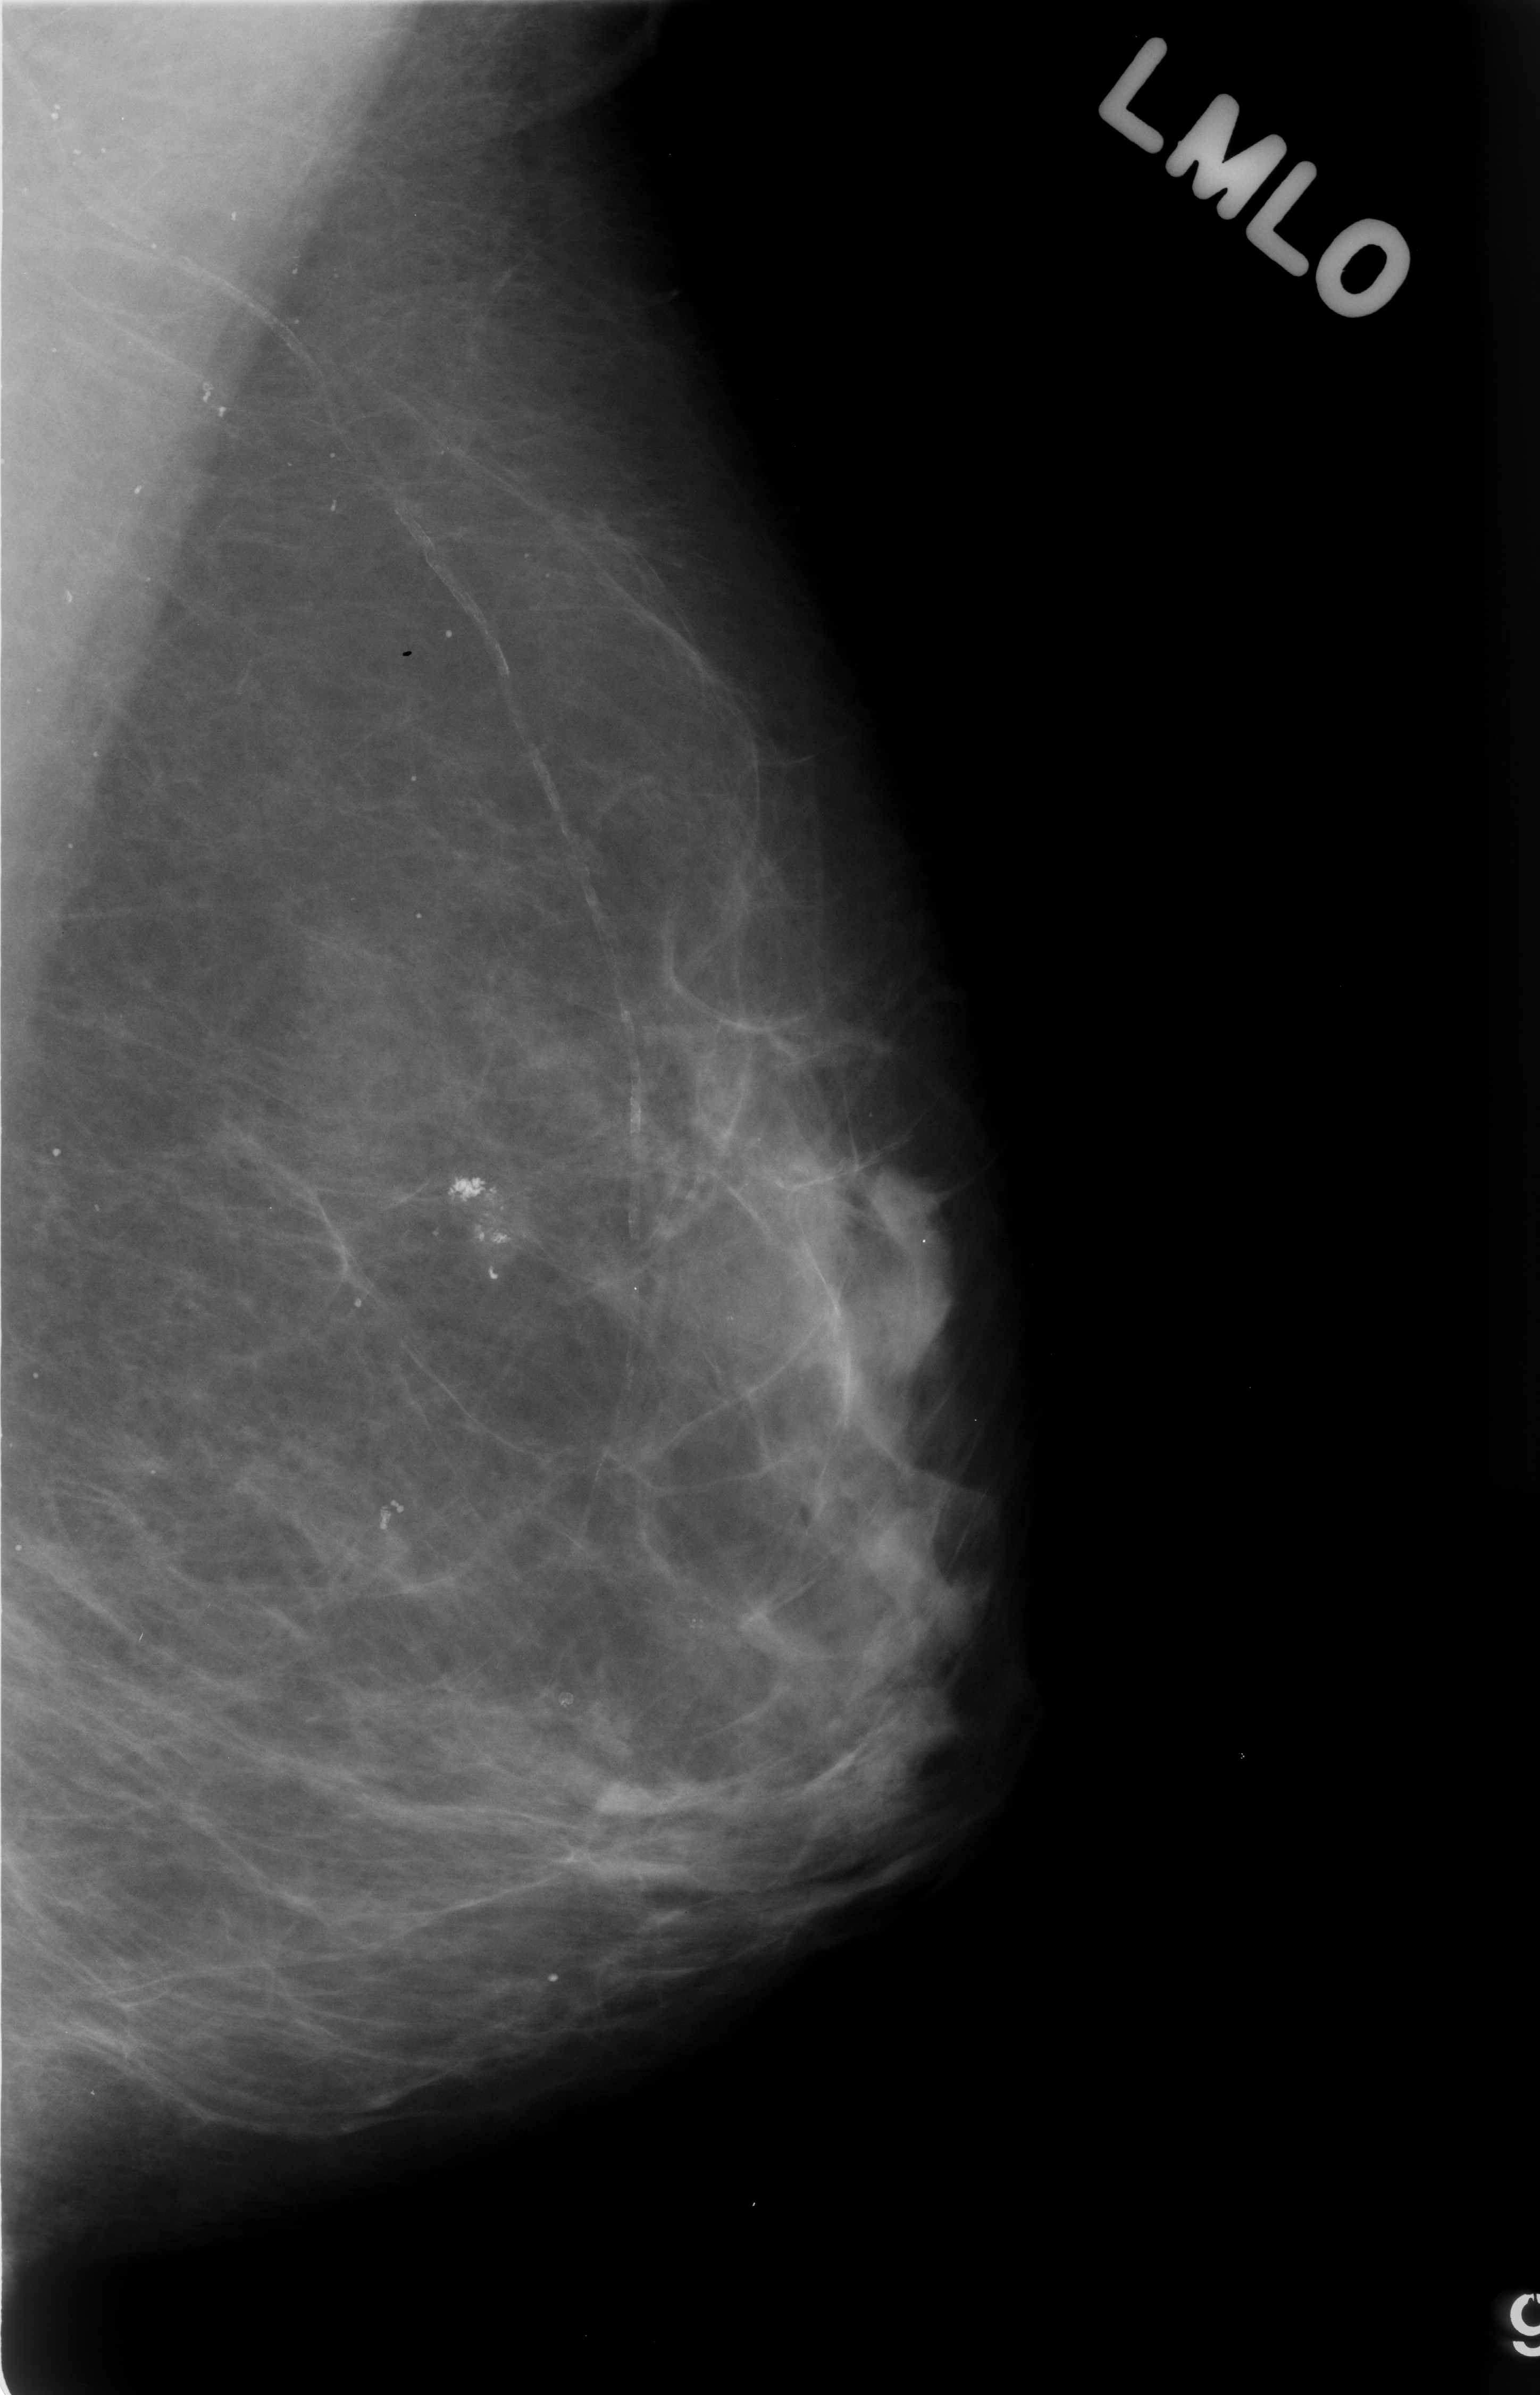
Scanned film-screen mammogram, left breast, MLO view.
- Radiologist-marked abnormalities on this image: calcifications, morphology pleomorphic, distribution clustered; BI-RADS assessment category 3; pathology (as recorded): benign.